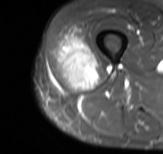
MRI of an extremity soft-tissue mass, one axial slice. Position 27 of 61 along the scan axis. STIR. MR volume resampled by the dataset authors to the PET/CT grid (not the native acquisition matrix). 3.27 mm slice thickness. 163 × 154 image matrix. Male patient. Case-level facts recorded for this patient, not image findings: histological type: poorly differentiated synovial sarcoma; grade: high; site of the primary tumour: right buttock.
Annotated regions visible in this slice (expert contour drawn on MRI and transferred to this co-registered scan by the dataset authors):
- gross tumour volume including surrounding oedema: box from (x=55, y=27) to (x=101, y=90) px
- gross tumour volume (mass): (x=57, y=36)–(x=99, y=90)